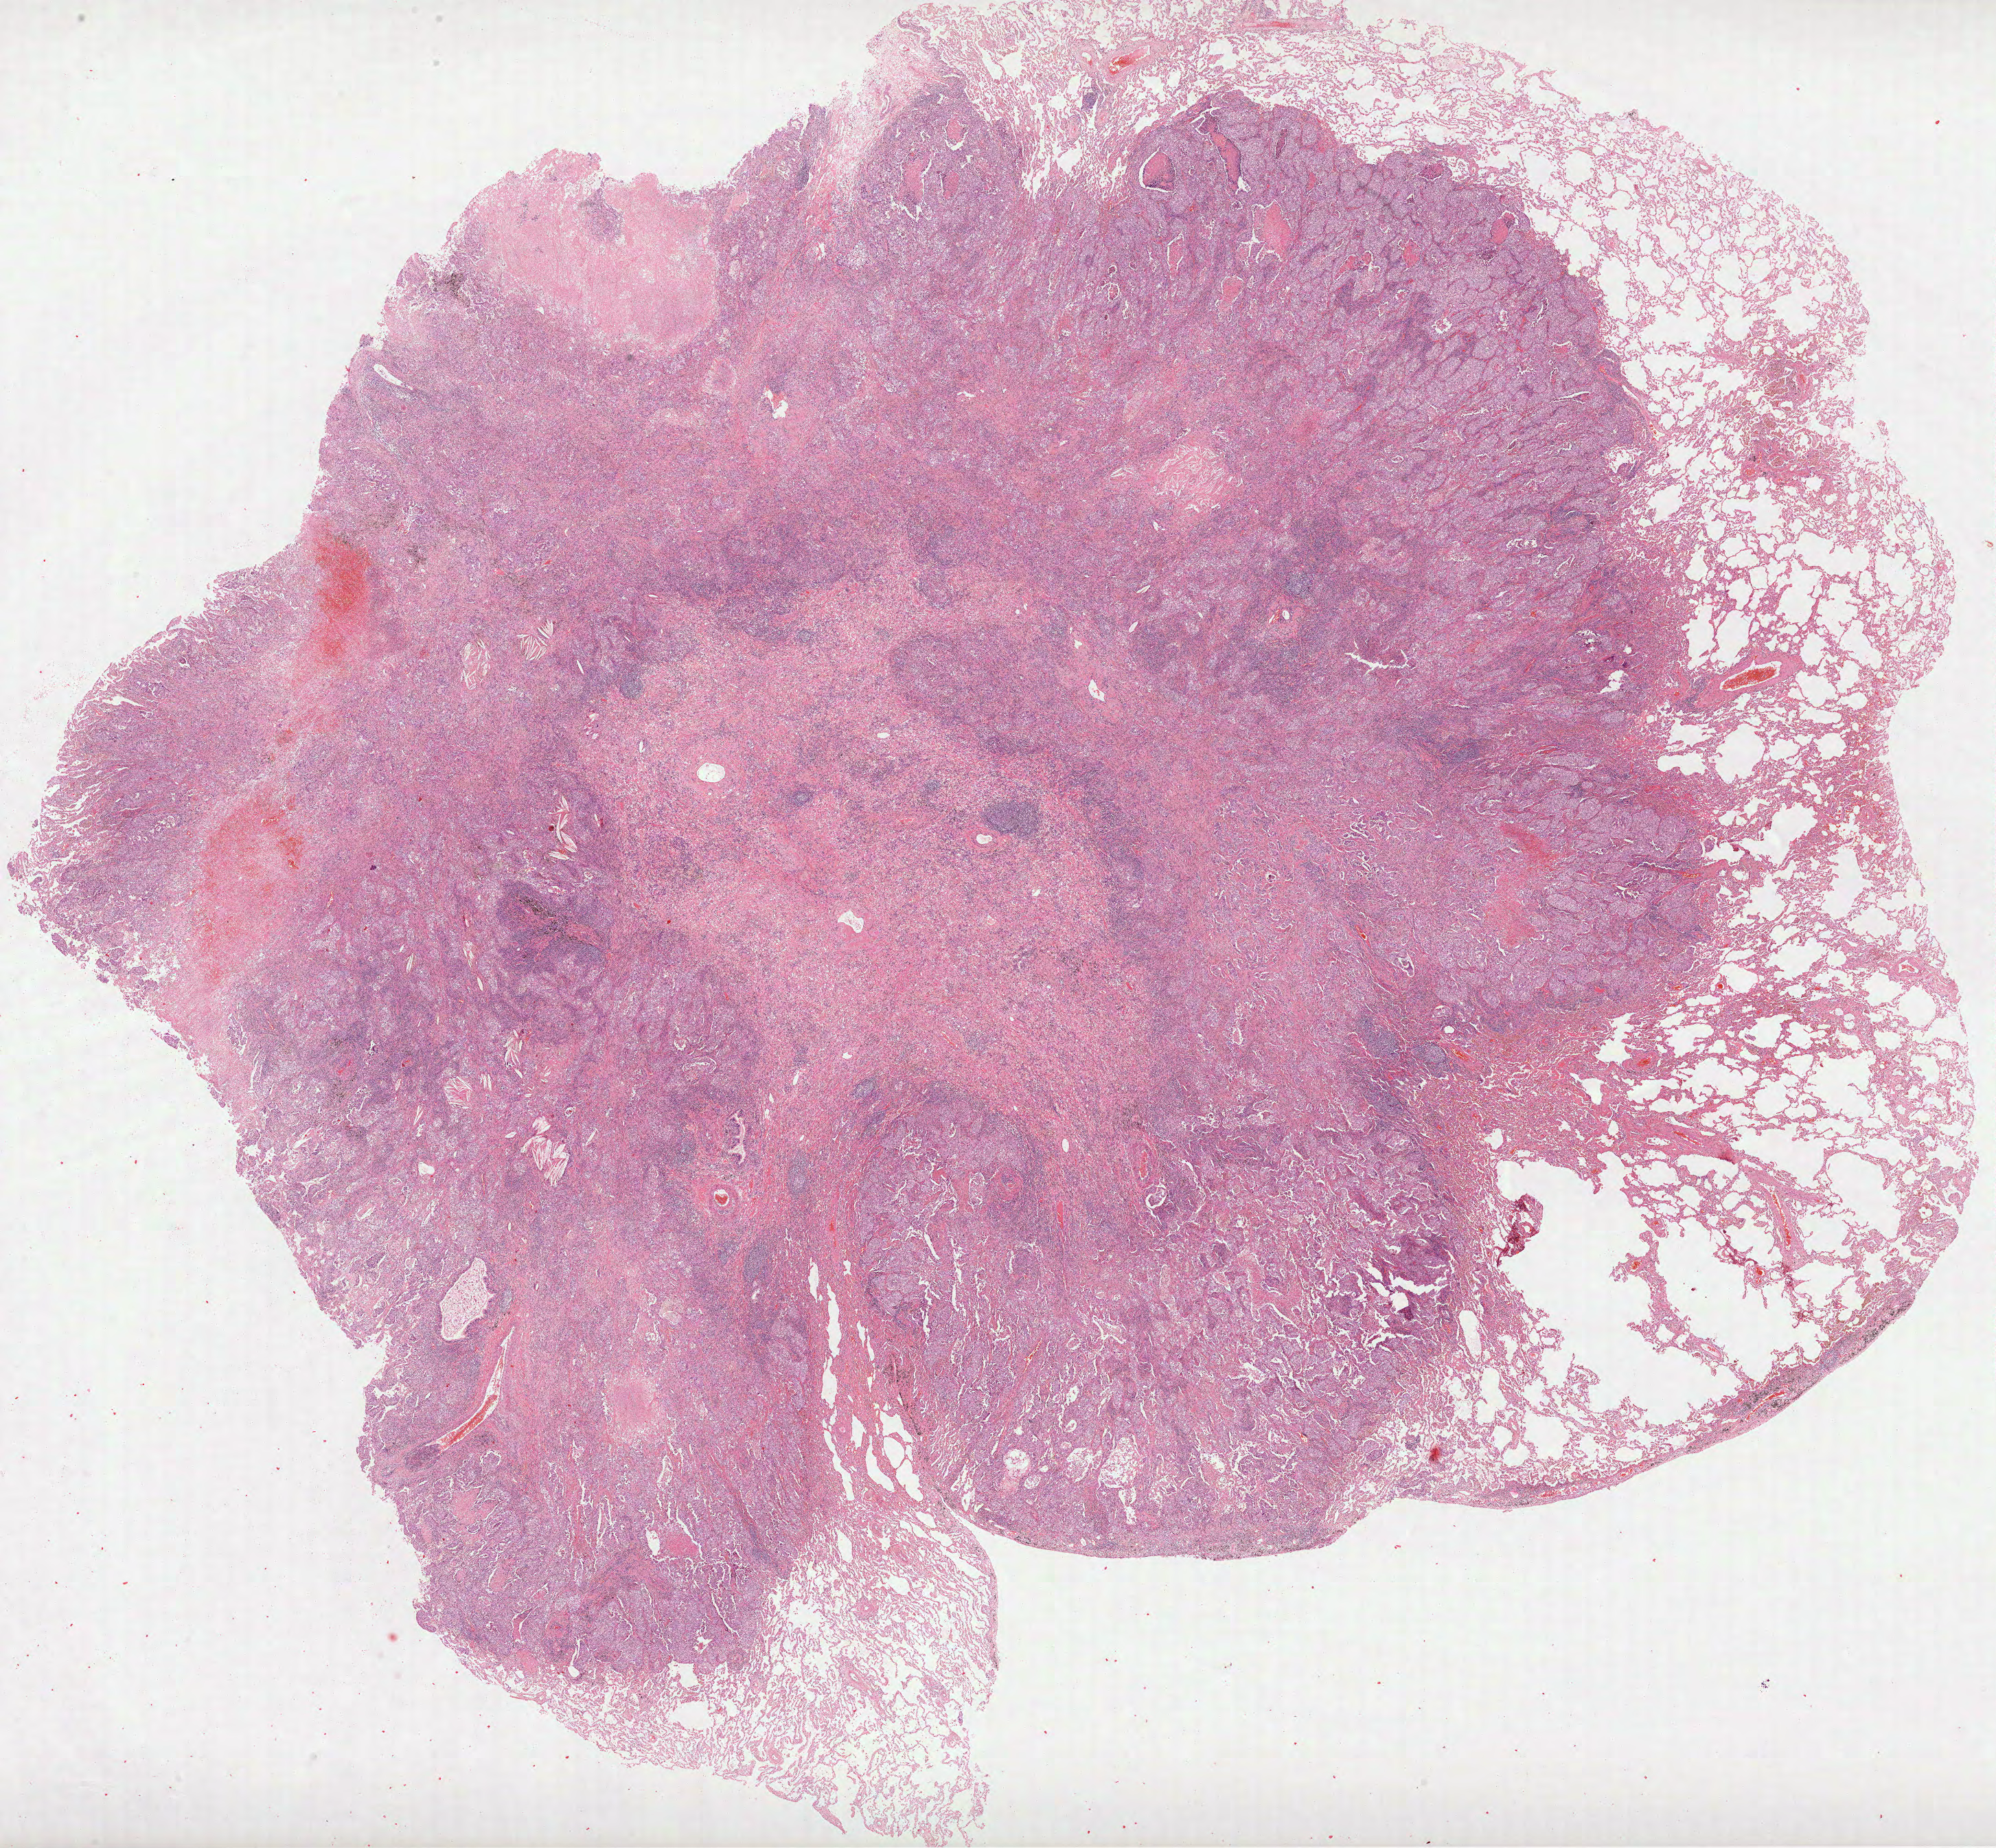
Hematoxylin and eosin (H&E) stained whole-slide image, a low-resolution overview of the entire scanned area, about 23.4 x 21.7 mm, FFPE section, primary tumour sample from the lung. Male patient; age at initial diagnosis 57 years.
Diagnosis: Solid carcinoma, NOS (upper lobe, lung). AJCC pathologic stage: IB (7th edition).